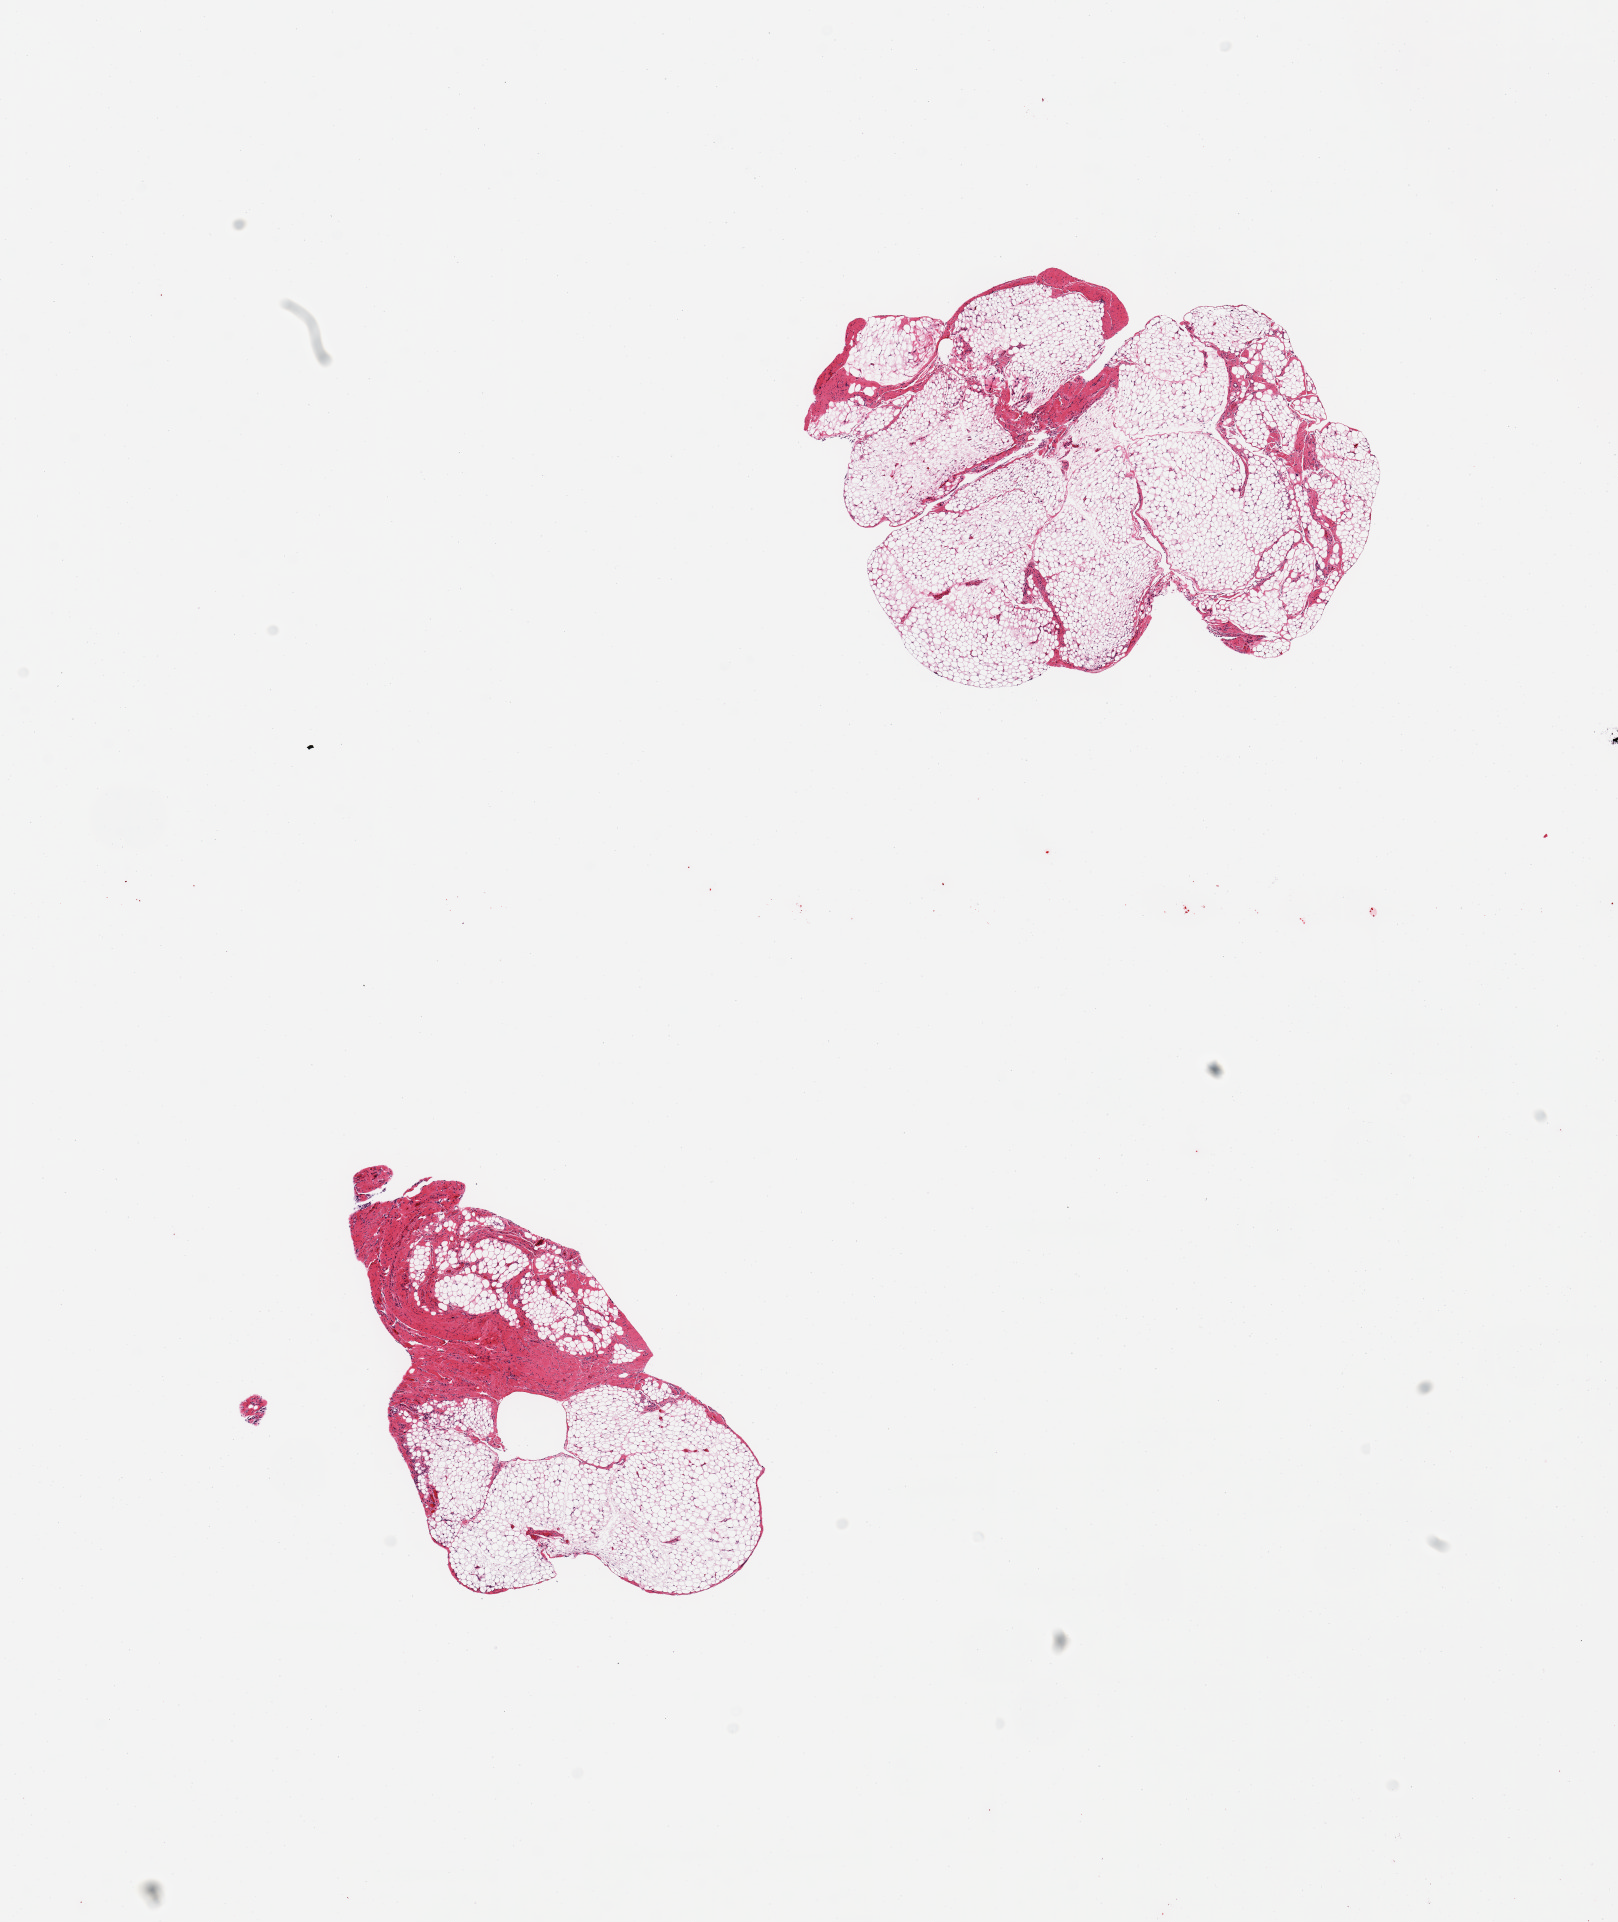
Hematoxylin and eosin (H&E) whole-slide image — a low-resolution overview of the entire scanned area, about 12.8 x 15.2 mm. PAXgene-fixed paraffin-embedded (PFPE) section. Section of omentum (target tissue). Tissue donor sample. Donor: female.
Review note (as recorded): 2 pieces; smaller piece has 30% fibrous content.